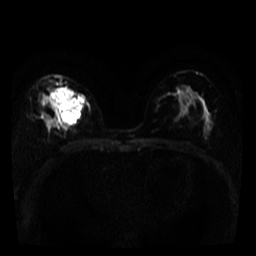
Breast MRI, one axial slice; position 21 of 39 along the scan axis; diffusion-weighted series; image 2 of 4 stored at this slice position (different b-values; order by instance number); 3 T; 5 mm slice thickness; 256 × 256 image matrix. Female patient.
Outlined on this slice (expert manual segmentation):
- tumour on diffusion-weighted imaging: bounding box [x1, y1, x2, y2] px = [47, 87, 87, 127]